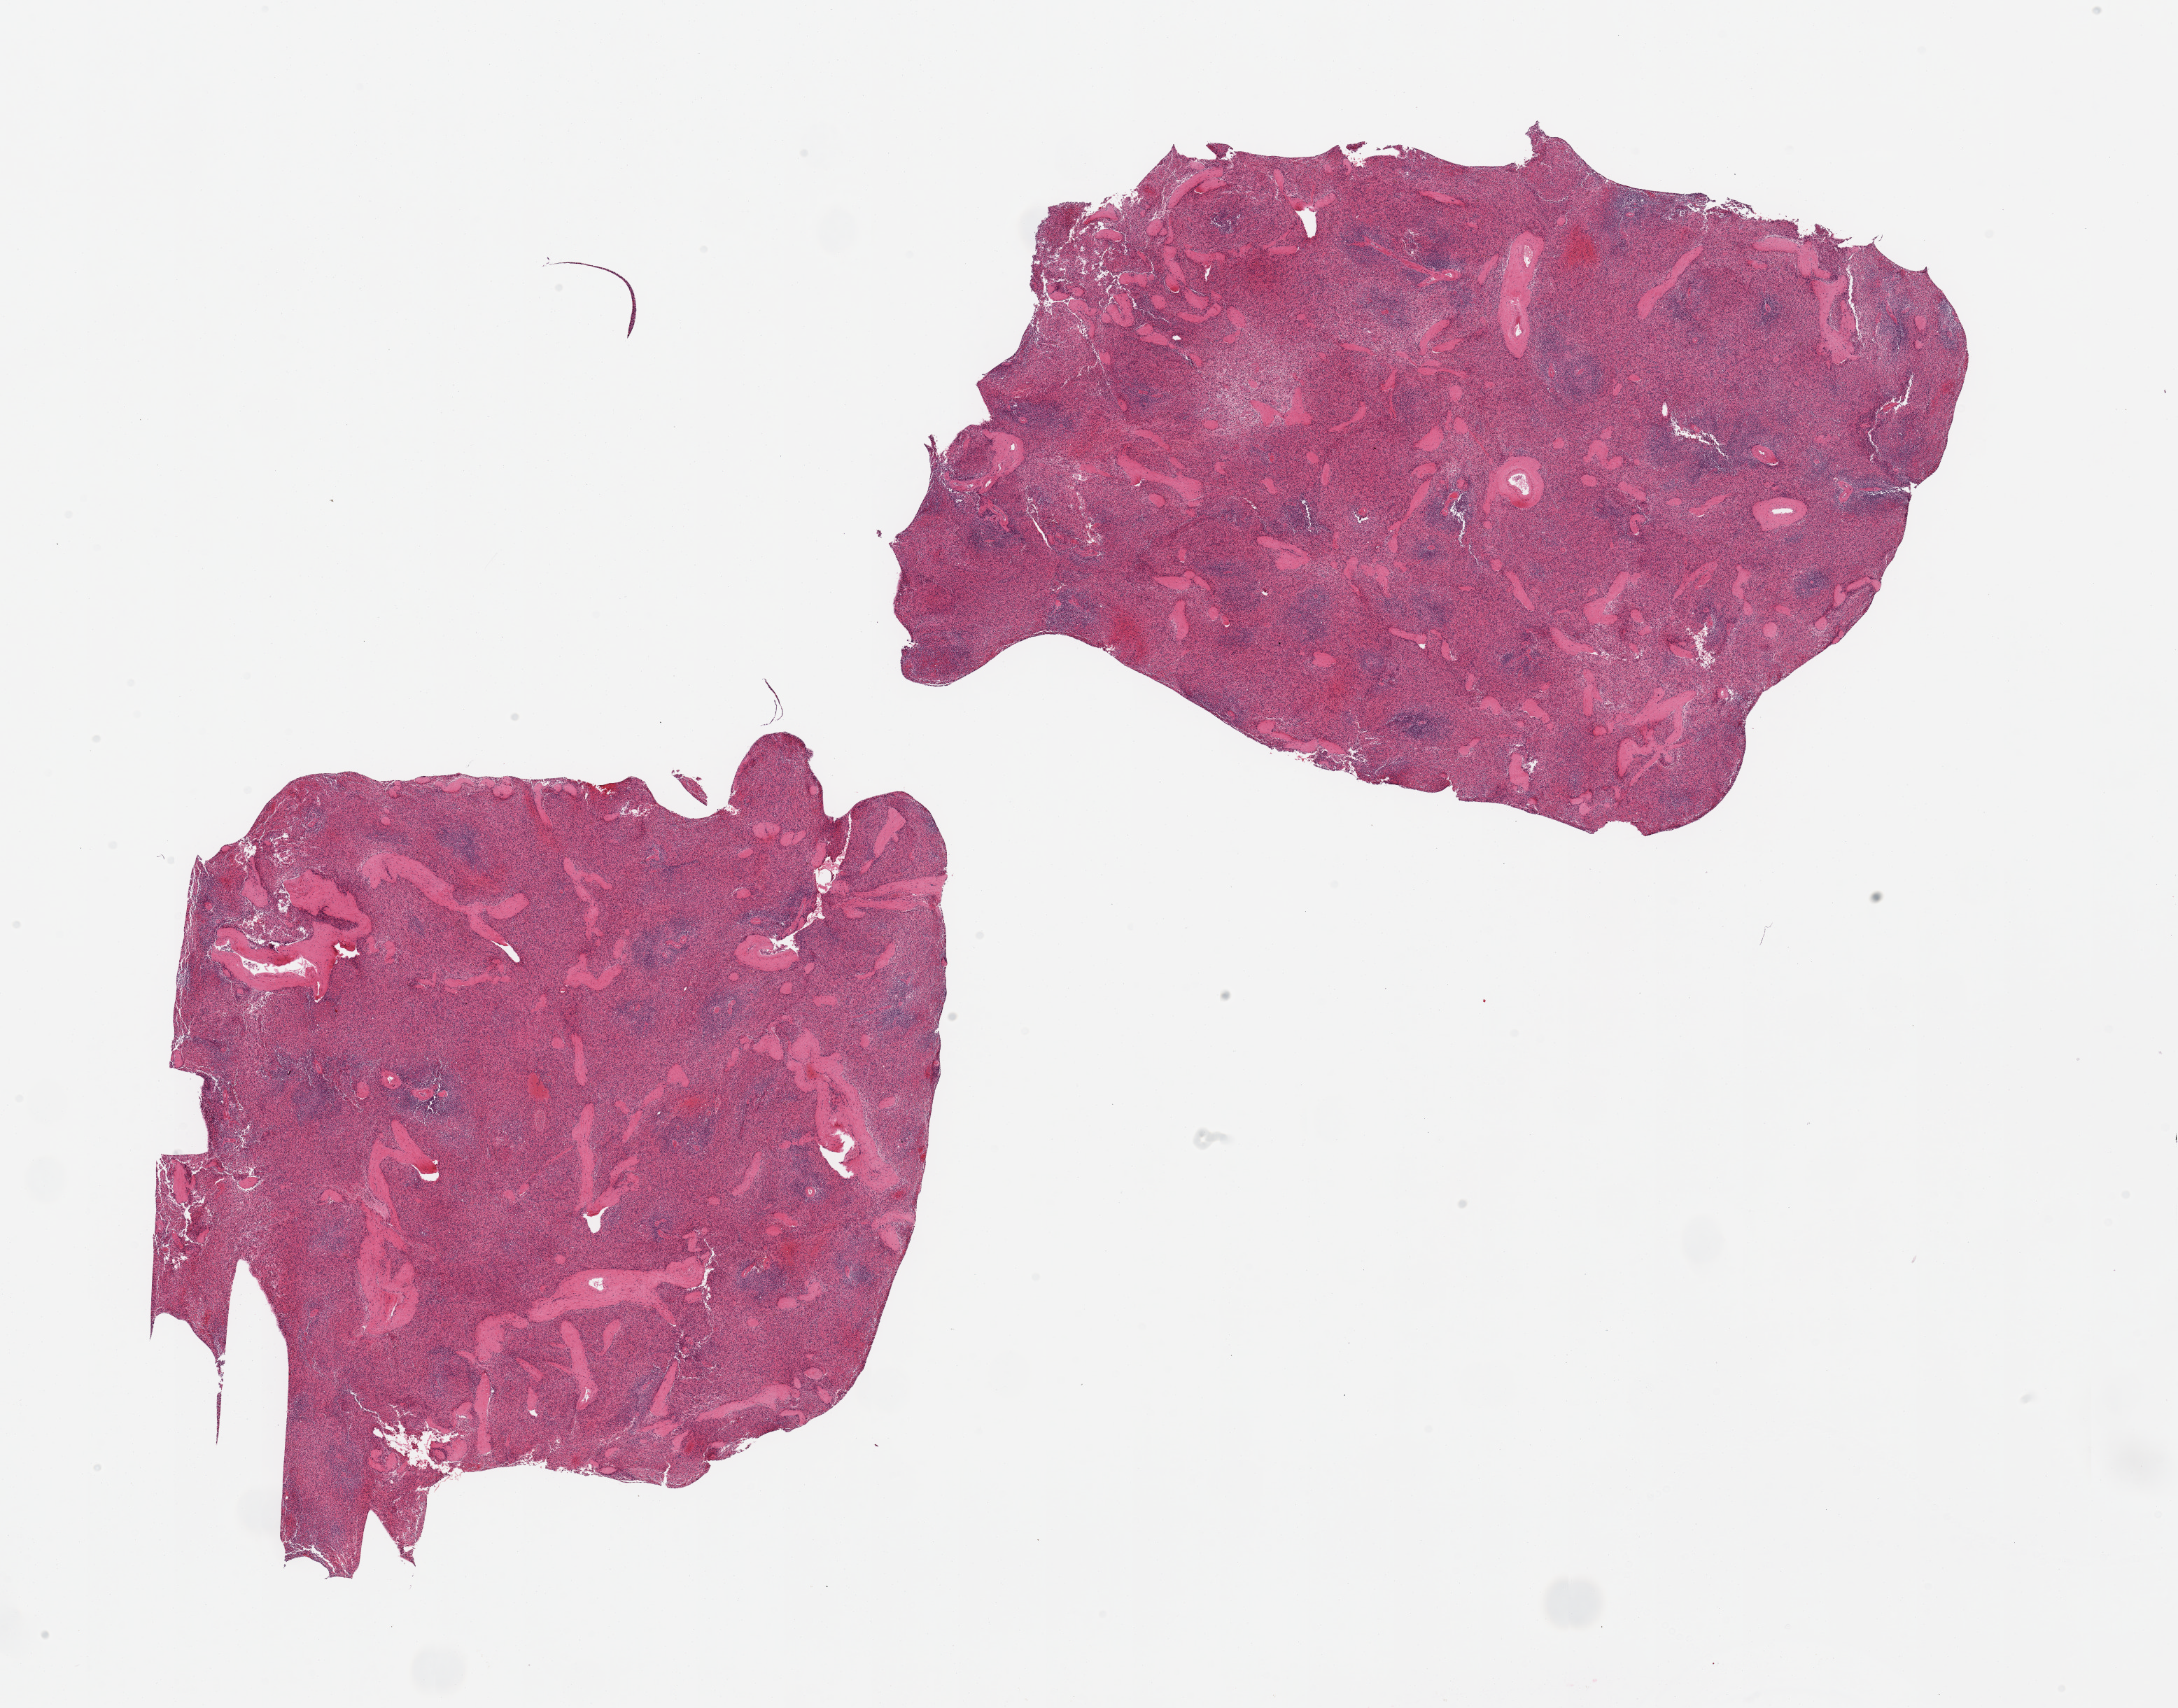
Digitized hematoxylin and eosin (H&E)-stained section, brightfield — shown as a low-resolution overview of the whole scanned area (about 24.6 x 19.3 mm), PAXgene-fixed, paraffin-embedded tissue, section of spleen (target tissue), donor tissue sample. Donor: male.
• review note (as recorded): 2 pieces, moderate congestion